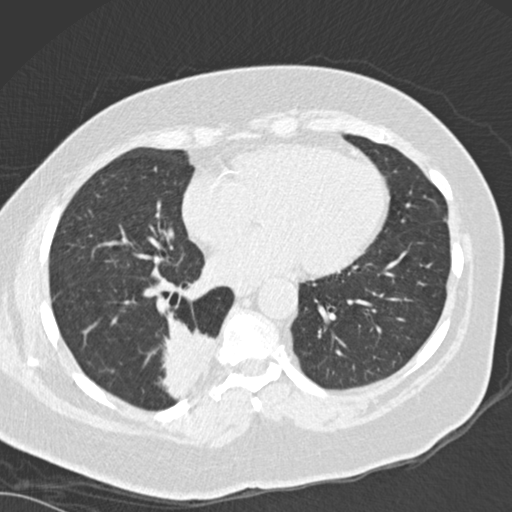
Low-dose screening chest CT, one axial slice; position 64 of 162 along the scan axis; reconstruction kernel B30f; lung window (W 1500 / L -600 HU); 2 mm slice thickness; 512 × 512 image matrix, field of view 328 × 328 mm.
Structures marked on this image (expert manual segmentation):
- lesion 1 (tumor, lower lobe of right lung): box from (x=159, y=312) to (x=215, y=400) px